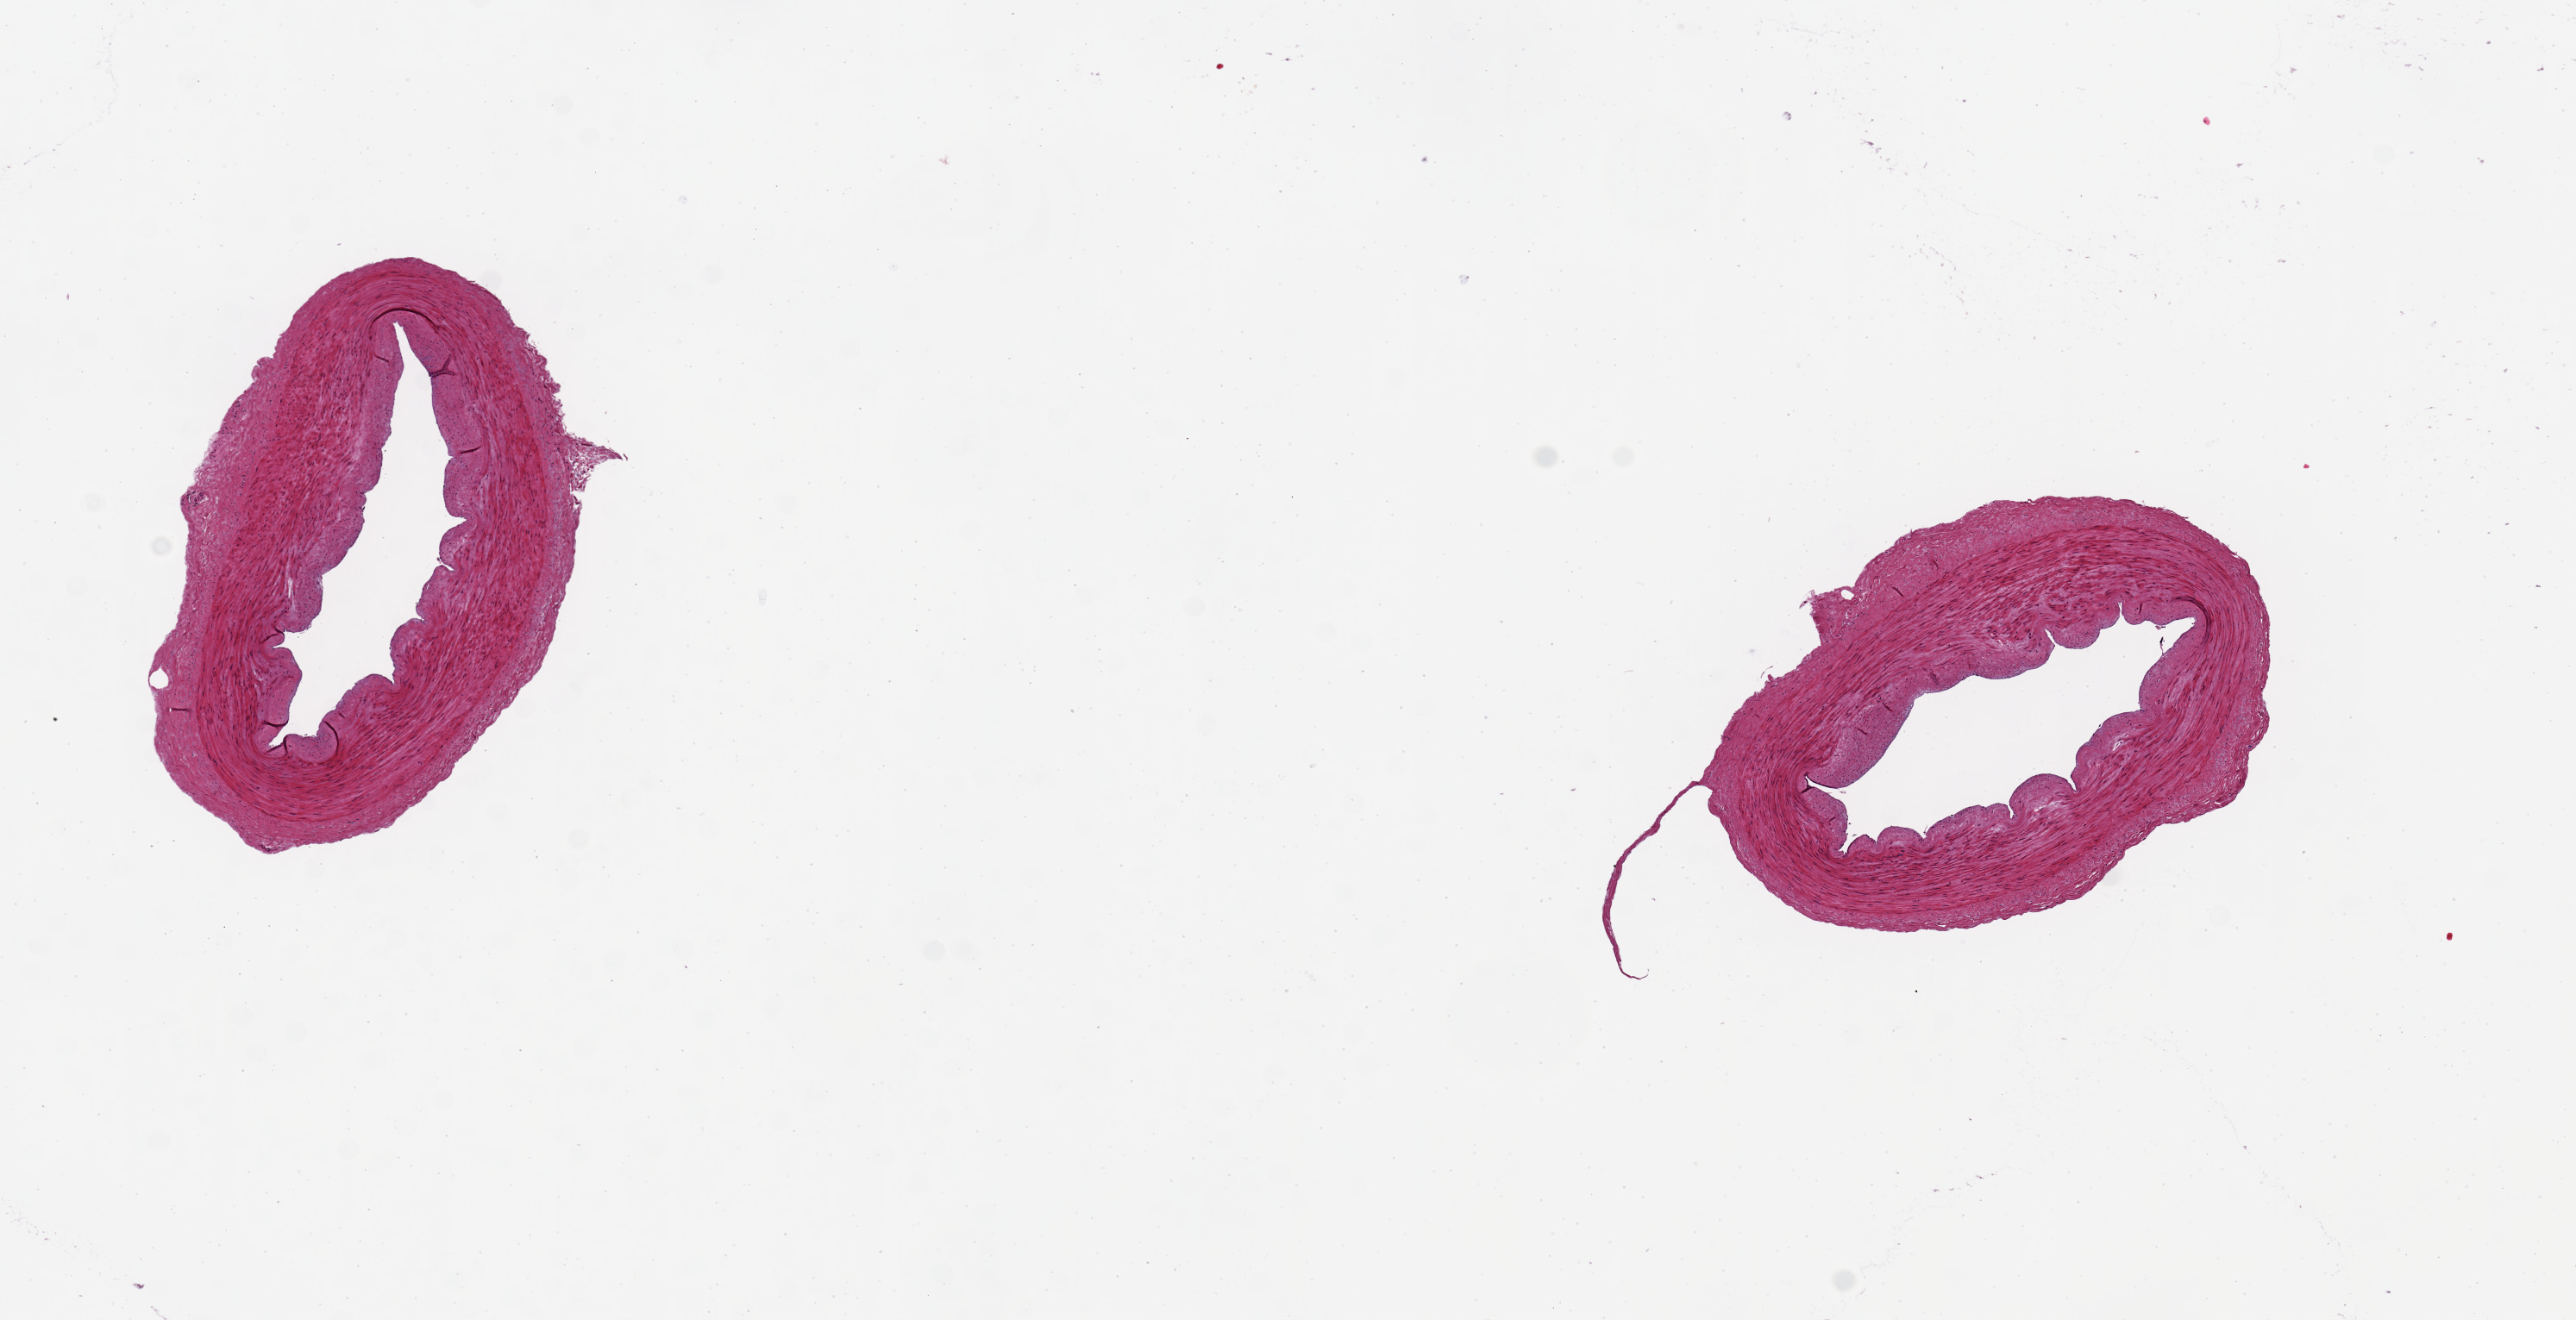
Whole-slide image, H&E stain — whole scanned area (about 11.8 x 6.1 mm) shown as a low-resolution overview. PAXgene-fixed, paraffin-embedded tissue. Target tissue: tibial artery. Donor tissue sample. Male donor.
- review note (as recorded): 2 aliquots. Good clean specimen, minimal adherent fat